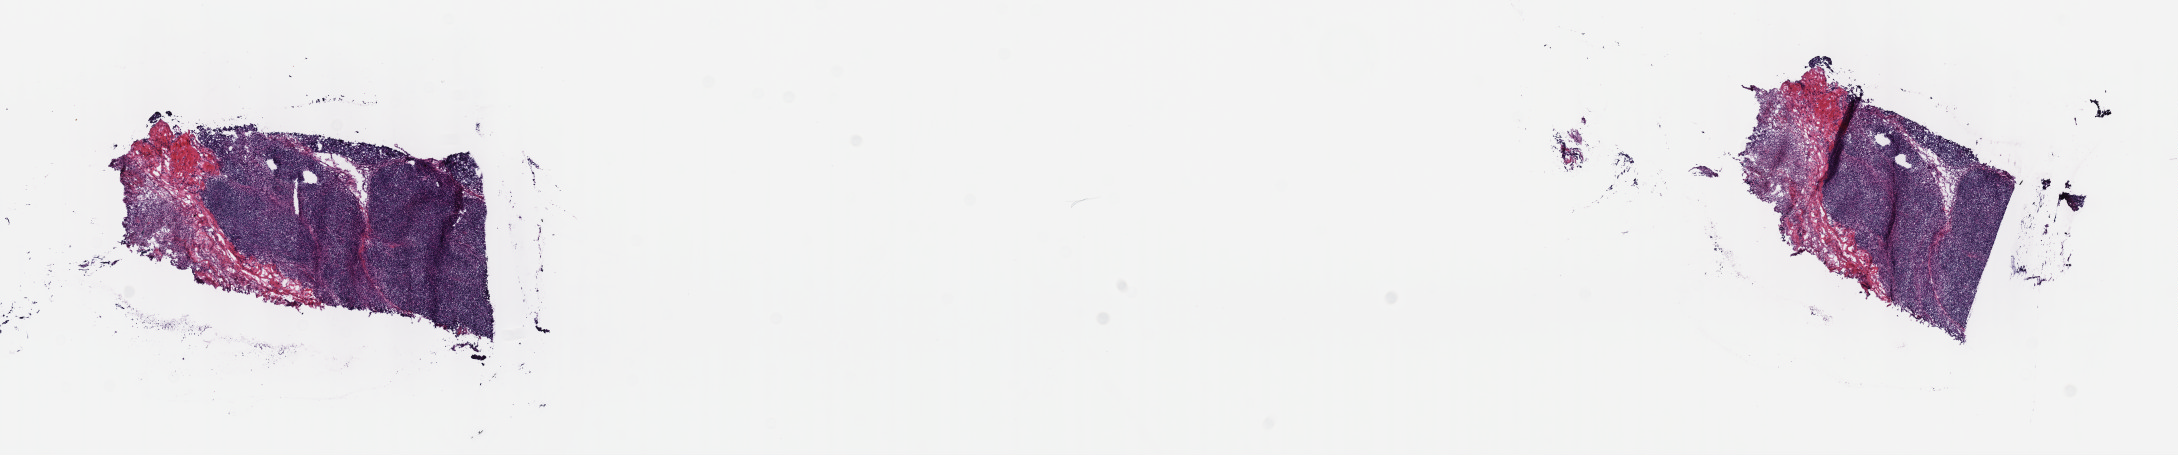
H&E-stained whole-slide image — low-resolution overview of the scanned area, about 17.6 x 3.7 mm (acquisition: 40x scan); frozen section; thymus, primary tumour sample. Male patient; age at initial diagnosis 67 years. Slide review estimates, as recorded: tumour cells 100%, tumour nuclei 75%, normal cells 0%, stromal cells 0%, necrosis 0%. Inflammatory infiltration, as recorded: lymphocyte infiltration 2%, monocyte infiltration 0%, neutrophil infiltration 0%.
Histologic diagnosis: Thymoma, type B2, malignant.